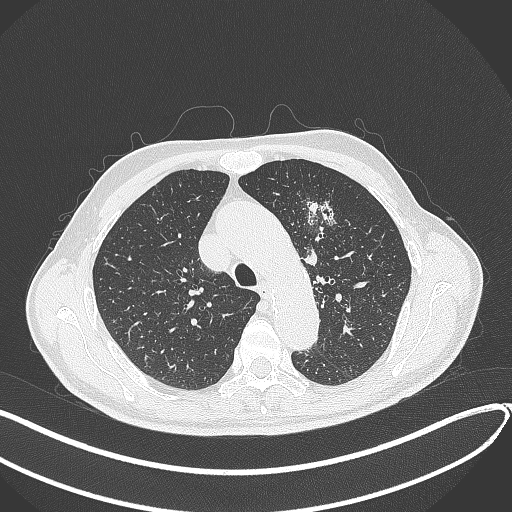
Chest CT, one axial slice; slice 302 of 459 in the series (ordered by position); 120 kVp; lung window (W 1500 / L -600 HU); 1 mm slice thickness; 512 × 512 image matrix, field of view 400 × 400 mm. Male patient, age 74 years. From the clinical record (not read from this slice): clinical TNM (as recorded): T2b N0 M1c.
Annotated regions visible in this slice (rectangle marked by the reading radiologist):
- lung tumour (recorded histology: adenocarcinoma): box from (x=305, y=200) to (x=340, y=242) px